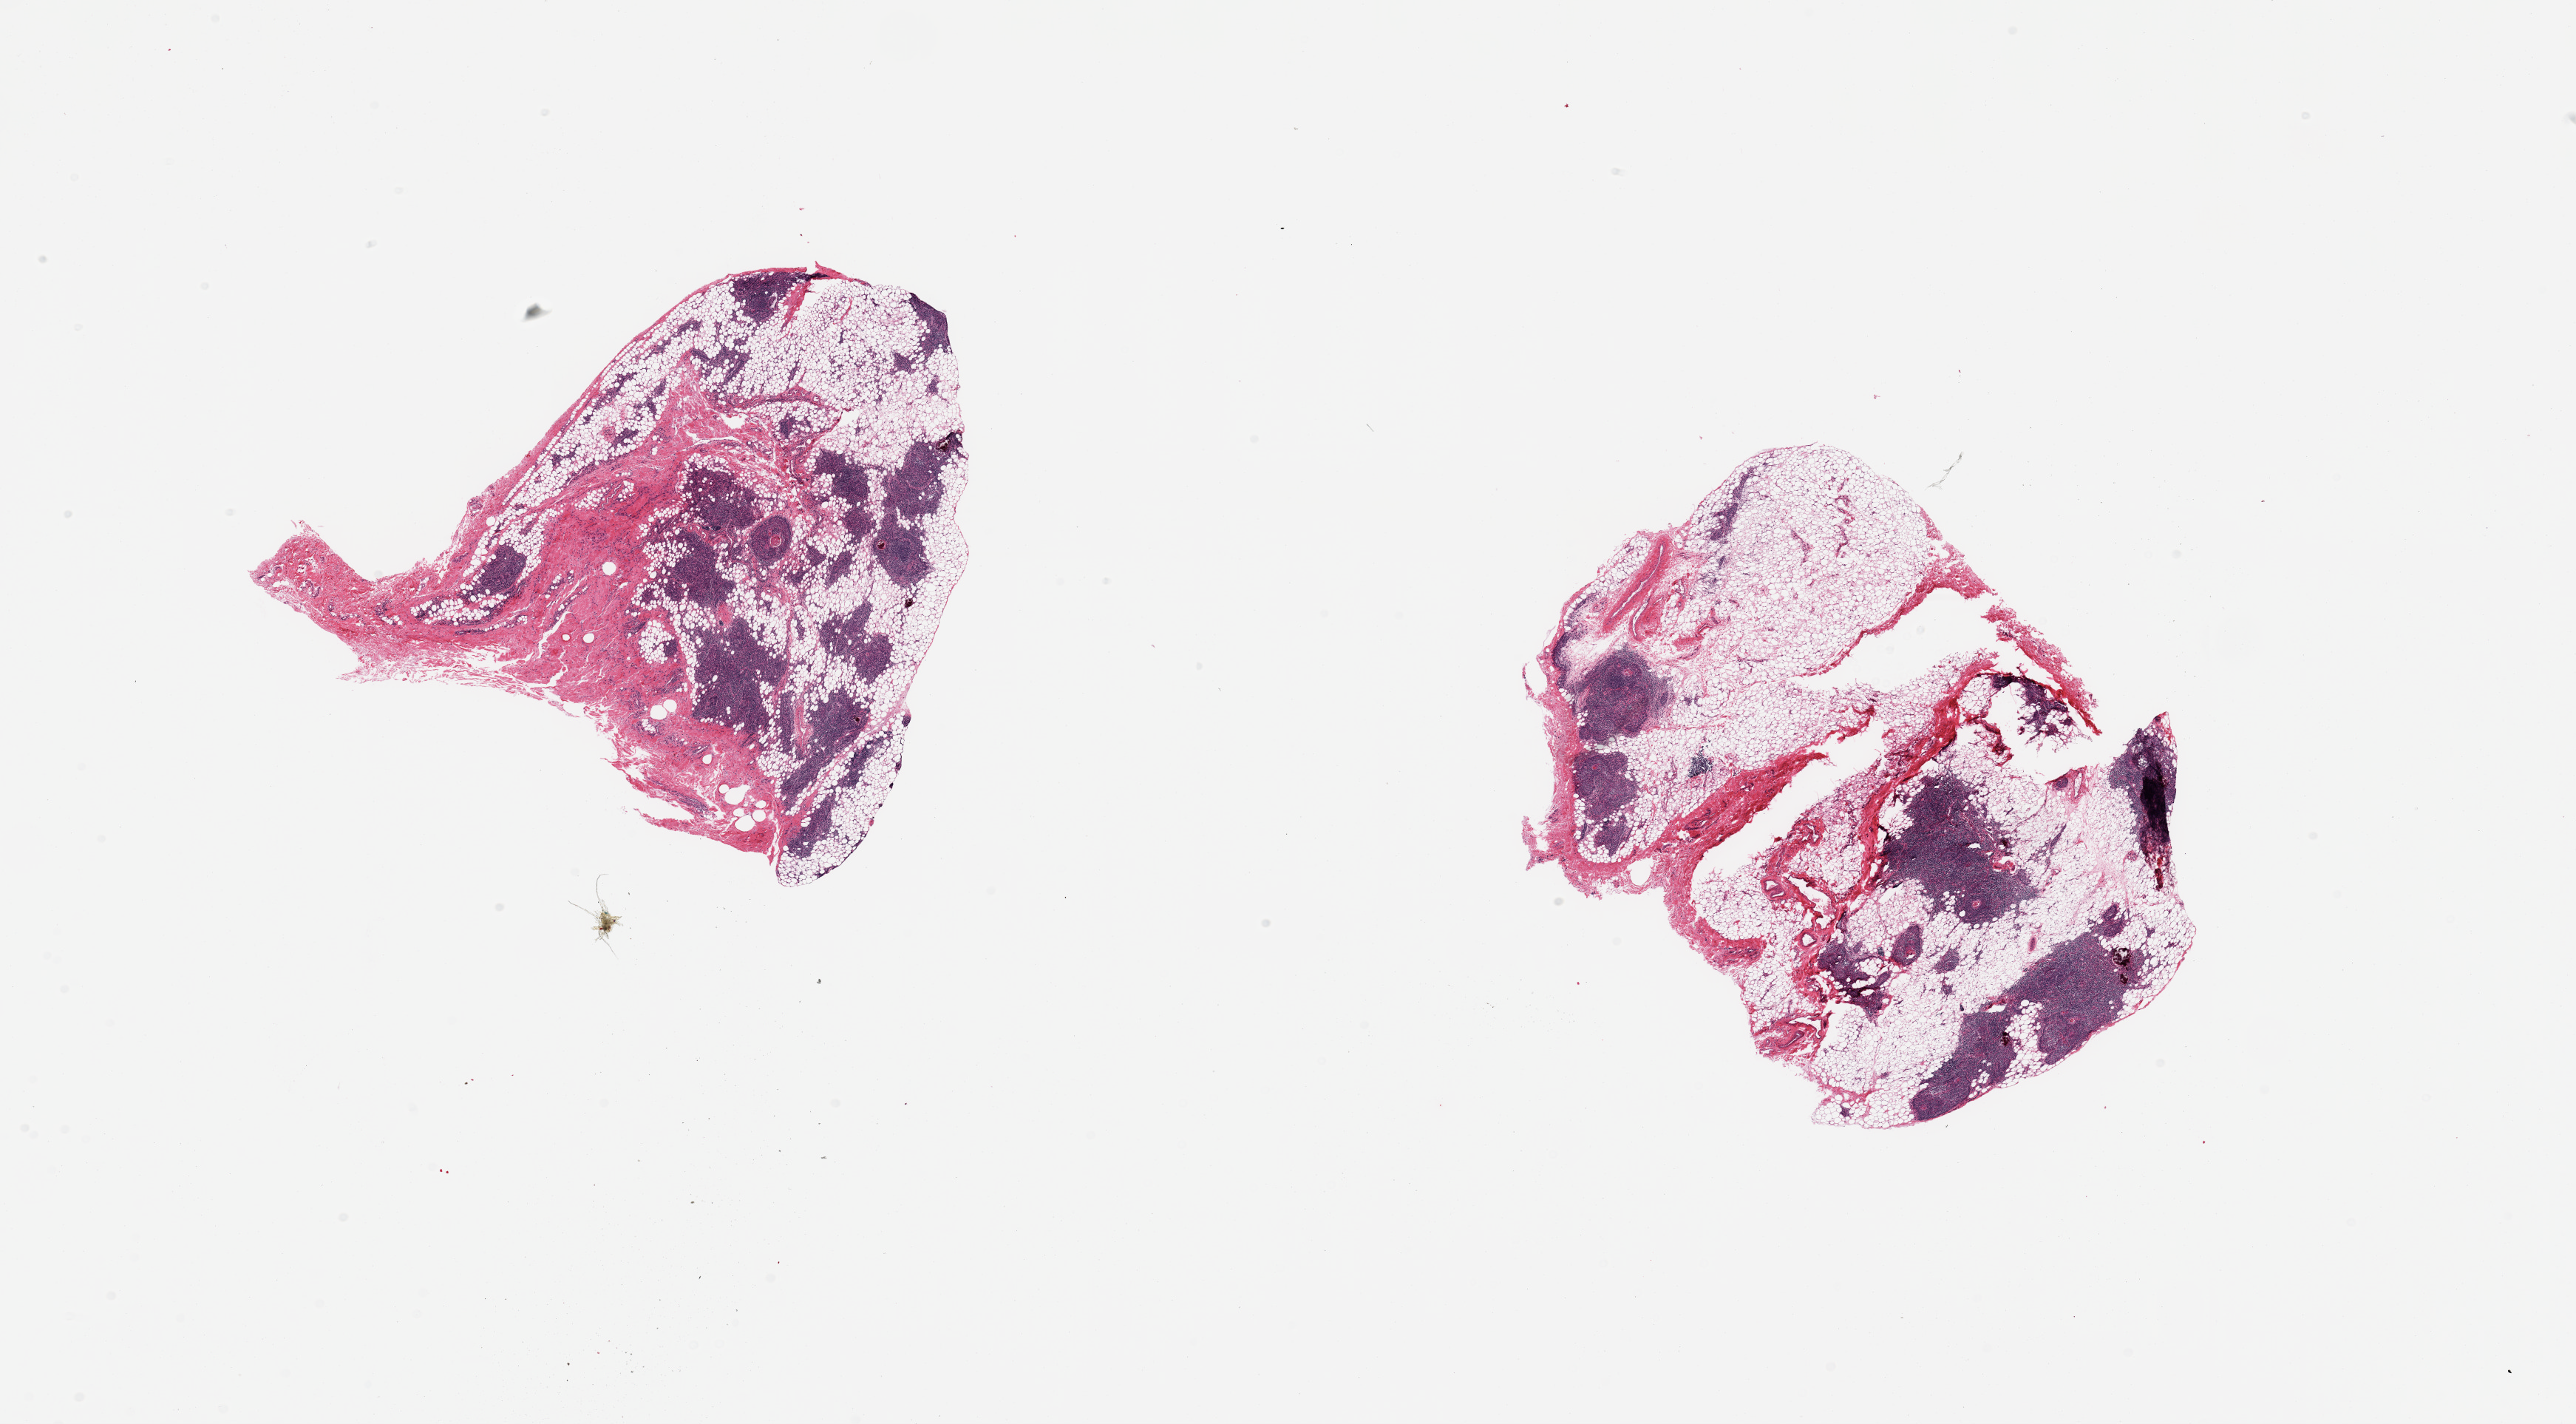
Haematoxylin and eosin whole-slide image, brightfield, low-resolution overview of the scanned area, about 27.6 x 15.2 mm (slide scanned at 20x); PAXgene-fixed, paraffin-embedded tissue; sampled site (target tissue): thyroid; tissue donor sample.
Review note (as recorded): 2 pieces, not thyroid; normal thymus.